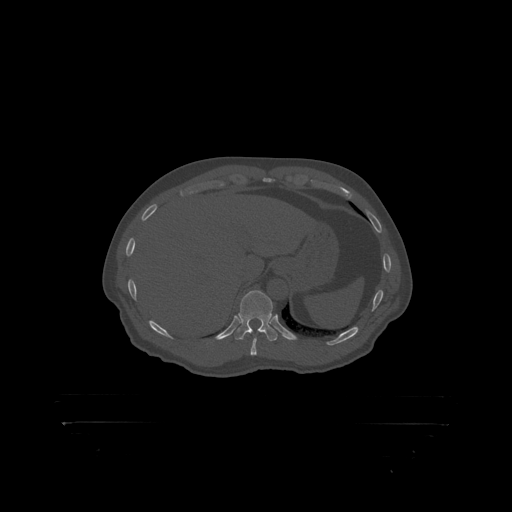
CT including the spine, one axial slice. Position 385 of 399 along the scan axis. 120 kVp. Bone window (W 1800 / L 400 HU). 512 × 512 image matrix, field of view 650 × 650 mm. Patient: male, 46 years. Case-level facts recorded for this patient, not image findings: primary cancer: skin.
Outlined on this slice (semi-automatically segmented with operator editing):
- T11 vertebra: bounding box [x1, y1, x2, y2] px = [239, 290, 273, 319]